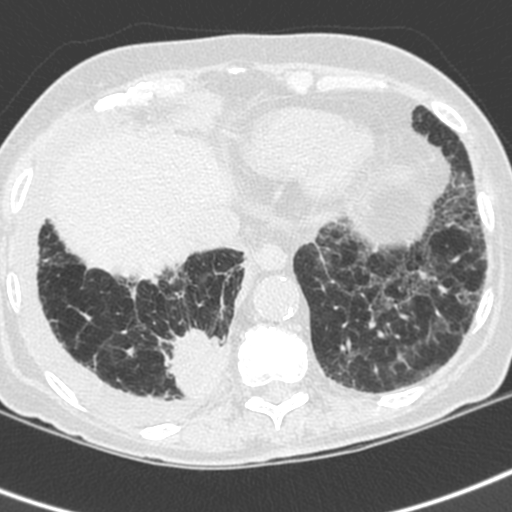
Low-dose screening chest CT, axial slice. Baseline screening round. Lung window (W 1500 / L -600 HU). 1.3 mm slice thickness. Slice 150 of 192 in the series. Female, age 73 years at enrolment.
Lesion marked by an expert reader, bounding box <159,324,235,406> (left, top, right, bottom; pixels). Reader record for this screening exam (exam-level; its link to the box is not recorded): non-calcified nodule or mass ≥4 mm, right lower lobe, 35 × 30 mm, spiculated (stellate) margins, soft tissue attenuation. Official screen result: positive, change unspecified: nodule(s) >= 4 mm or enlarging nodule(s), mass(es), or other non-specific abnormalities suspicious for lung cancer. Lung cancer was diagnosed 22 days after this screen: adenocarcinoma, NOS, right lower lobe, stage IV (AJCC 6th edition), 35 mm at pathology.